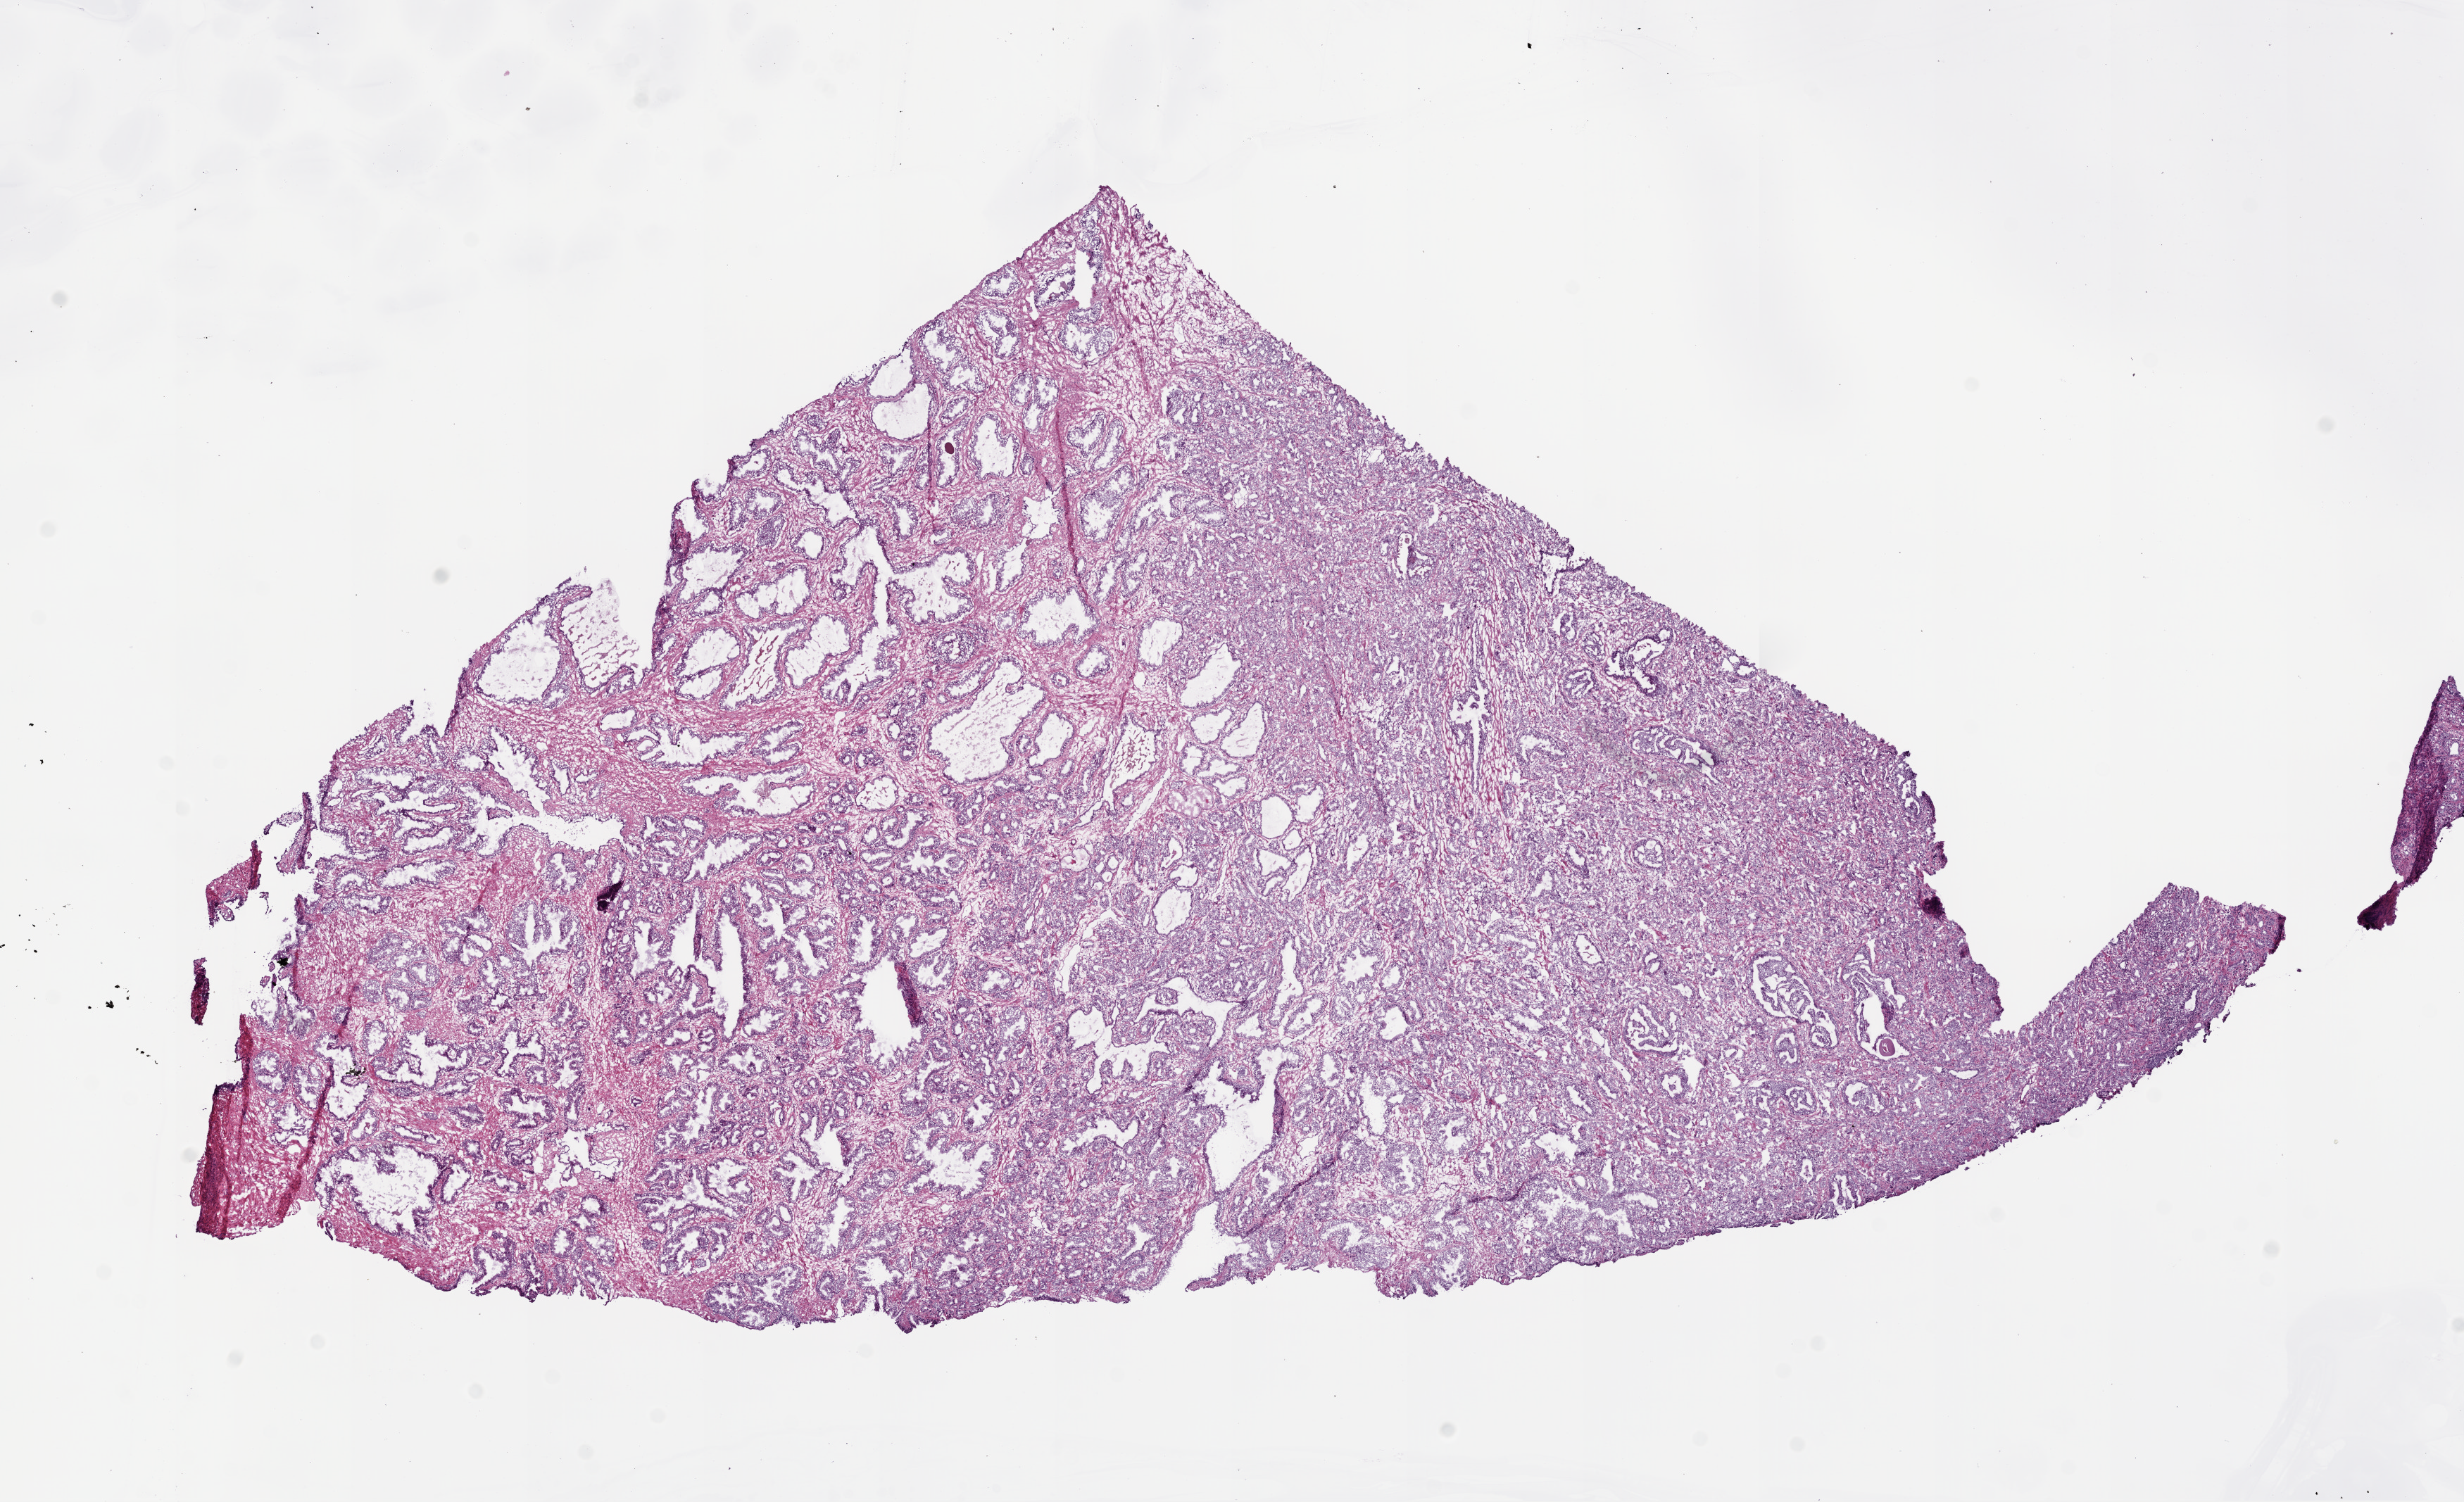
Hematoxylin and eosin (H&E) stained whole-slide image, shown as a low-resolution overview of the whole scanned area (about 14.0 x 8.6 mm, from a 20x scan); frozen section from the bottom of the tissue portion; prostate, primary tumour sample. Patient: male, age at initial diagnosis 48 years. Gleason score: 7 (4+3). Pathologist review of this section (percent, as recorded): tumour cells 50%, tumour nuclei 50%, normal cells 30%, stromal cells 20%, necrosis 0%. Infiltration values recorded for this section: lymphocyte infiltration 0%, monocyte infiltration 0%, neutrophil infiltration 0%.
Laterality: bilateral. Histologic diagnosis: Acinar cell carcinoma (prostate gland).